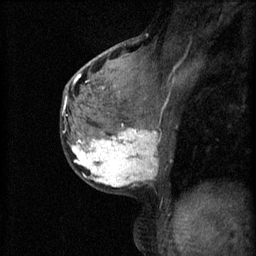
Breast MRI (dynamic contrast-enhanced), one sagittal slice. Position 33 of 60 along the scan axis. 3 images stored at this slice position (order not interpretable as contrast timing). 1.5 T. TE 4.2 ms, TR 11 ms. 2 mm slice thickness. 256 × 256 image matrix, field of view 180 × 180 mm. Patient: female, 37 years.
Annotated regions visible in this slice (semi-automatic segmentation, software-assisted and operator-edited):
- analysis volume of interest (the breast-tissue region the enhancement analysis was run in; not a lesion): bounding box (x1, y1, x2, y2) in pixels: (68, 118, 167, 195)
- tumour enhancement mask (voxels above the 70 % enhancement threshold inside the analysis volume of interest): (72, 124, 158, 187)